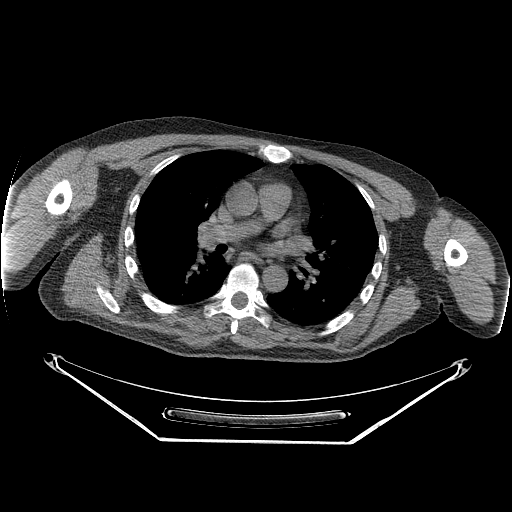
CT of an extremity soft-tissue mass (from a PET/CT study), one axial slice. Position 175 of 267 along the scan axis. Reconstruction kernel STANDARD. Soft-tissue window (W 400 / L 40 HU). 512 × 512 image matrix, field of view 500 × 500 mm. Male patient. From the clinical record (not read from this slice): histological type: pleiomorphic spindle cell undifferentiated; grade: high; site of the primary tumour: right parascapusular.
Structures marked on this image (expert contour drawn on MRI and transferred to this co-registered scan by the dataset authors):
- gross tumour volume including surrounding oedema: bounding box (x1, y1, x2, y2) in pixels: (160, 311, 225, 332)